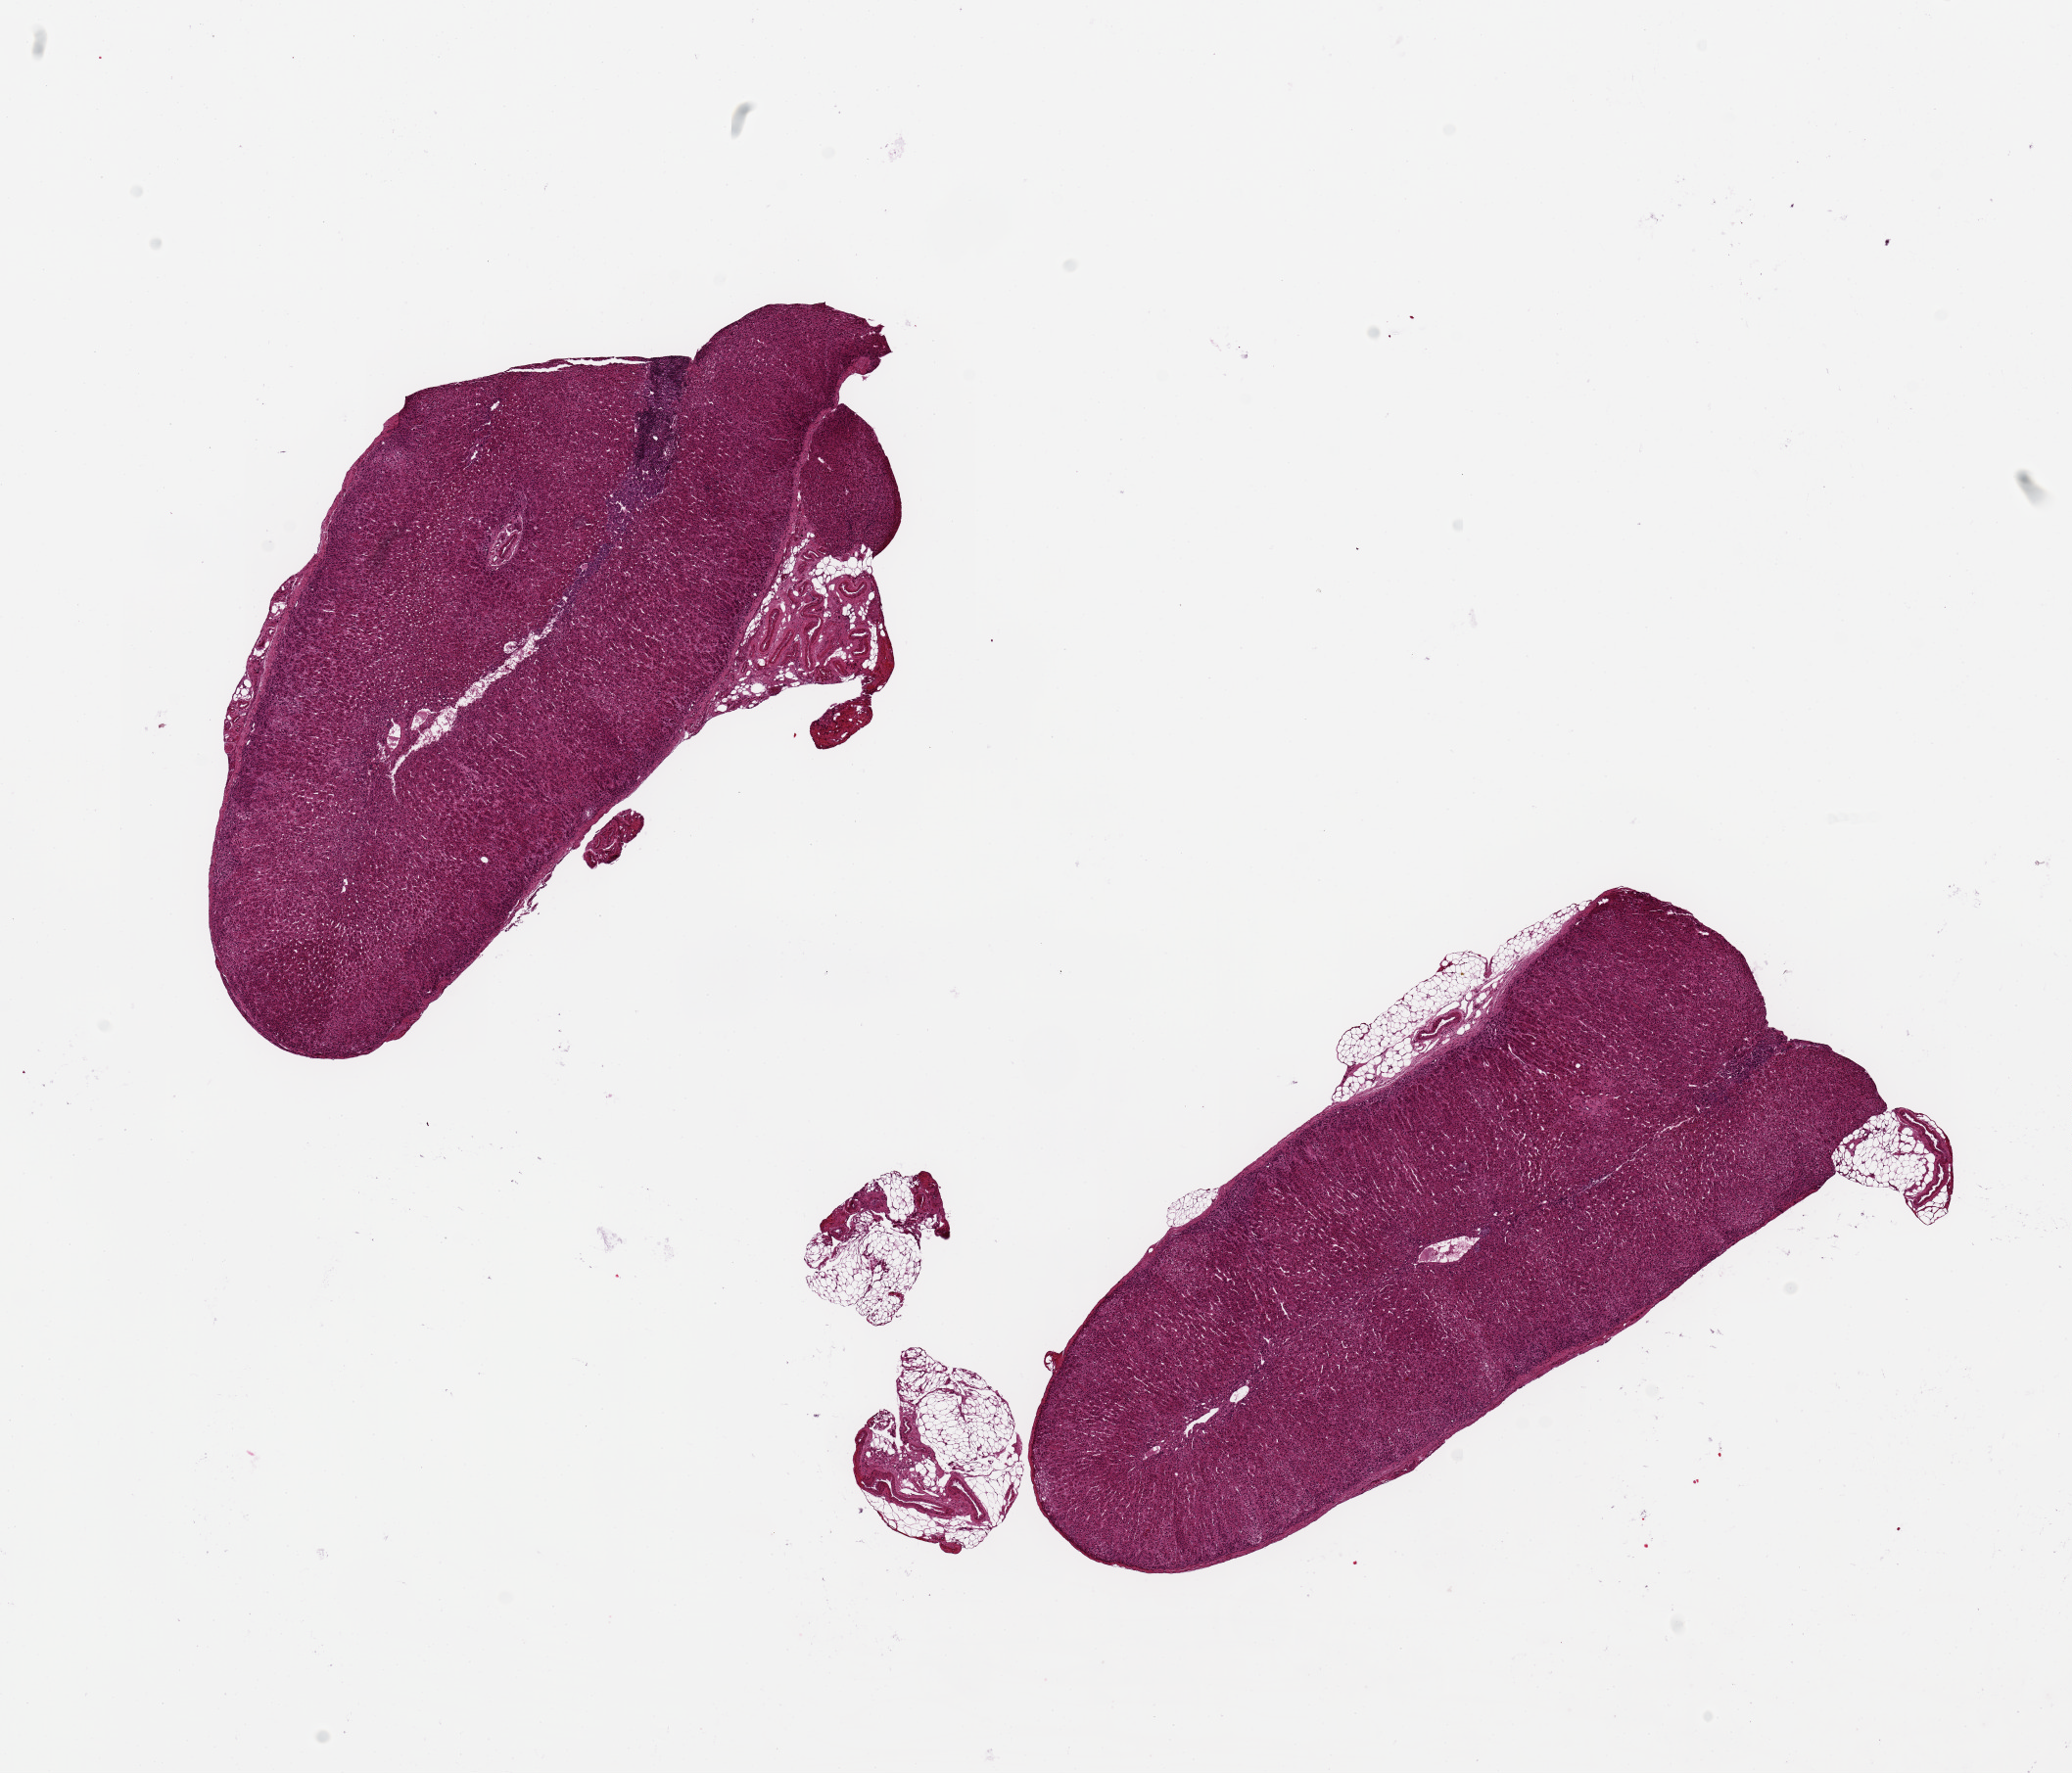
H&E whole-slide image — low-resolution overview of the scanned area, about 16.7 x 14.3 mm; PAXgene-fixed, paraffin-embedded tissue; section of adrenal gland (target tissue); tissue donor sample. Female donor.
Review note (as recorded): 2 pieces, 7x3 mm, cortex.